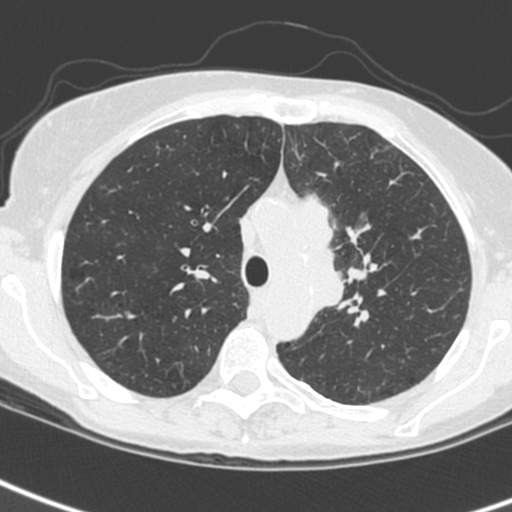
Low-dose screening chest CT, one axial slice. Slice 182 of 242 in the series (ordered by position). Lung window (W 1500 / L -600 HU). 1.3 mm slice thickness. 512 × 512 image matrix, field of view 284 × 284 mm.
Outlined on this slice (manually delineated by an expert):
- lesion 3 (tumor, upper lobe of left lung): bounding box [x1, y1, x2, y2] px = [300, 195, 344, 310]